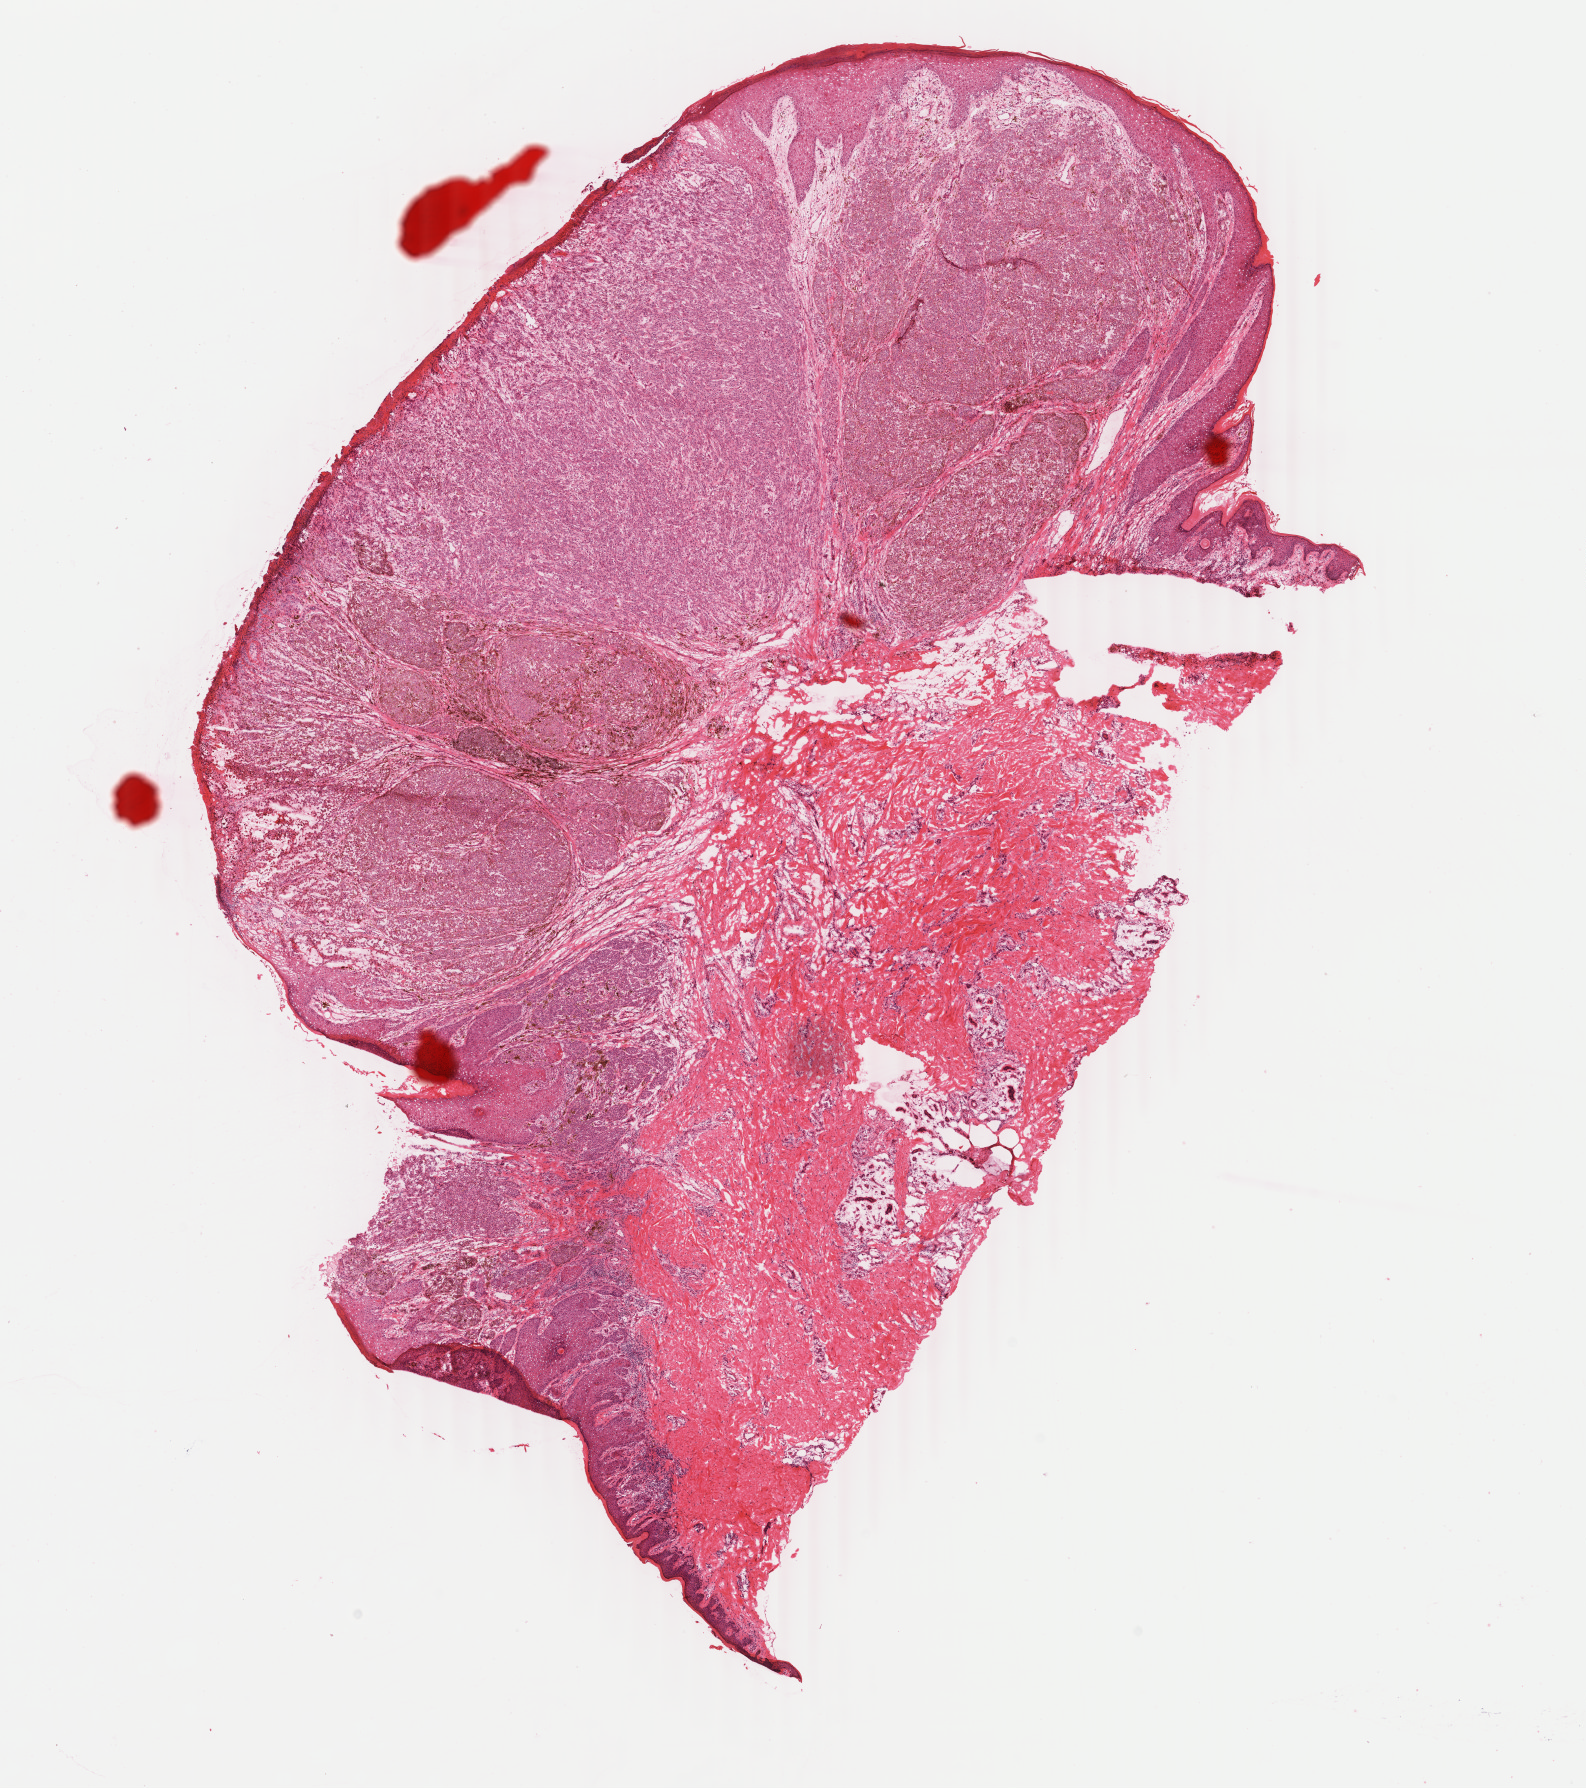
Whole-slide histology image, H&E — low-resolution overview of the scanned area, about 12.6 x 14.2 mm; FFPE section; sample: primary tumour, skin. Male, age 48 years at initial diagnosis.
TNM: T4b N0 M0. AJCC pathologic stage: IIC (7th edition). Pathologic diagnosis: Malignant melanoma, NOS.